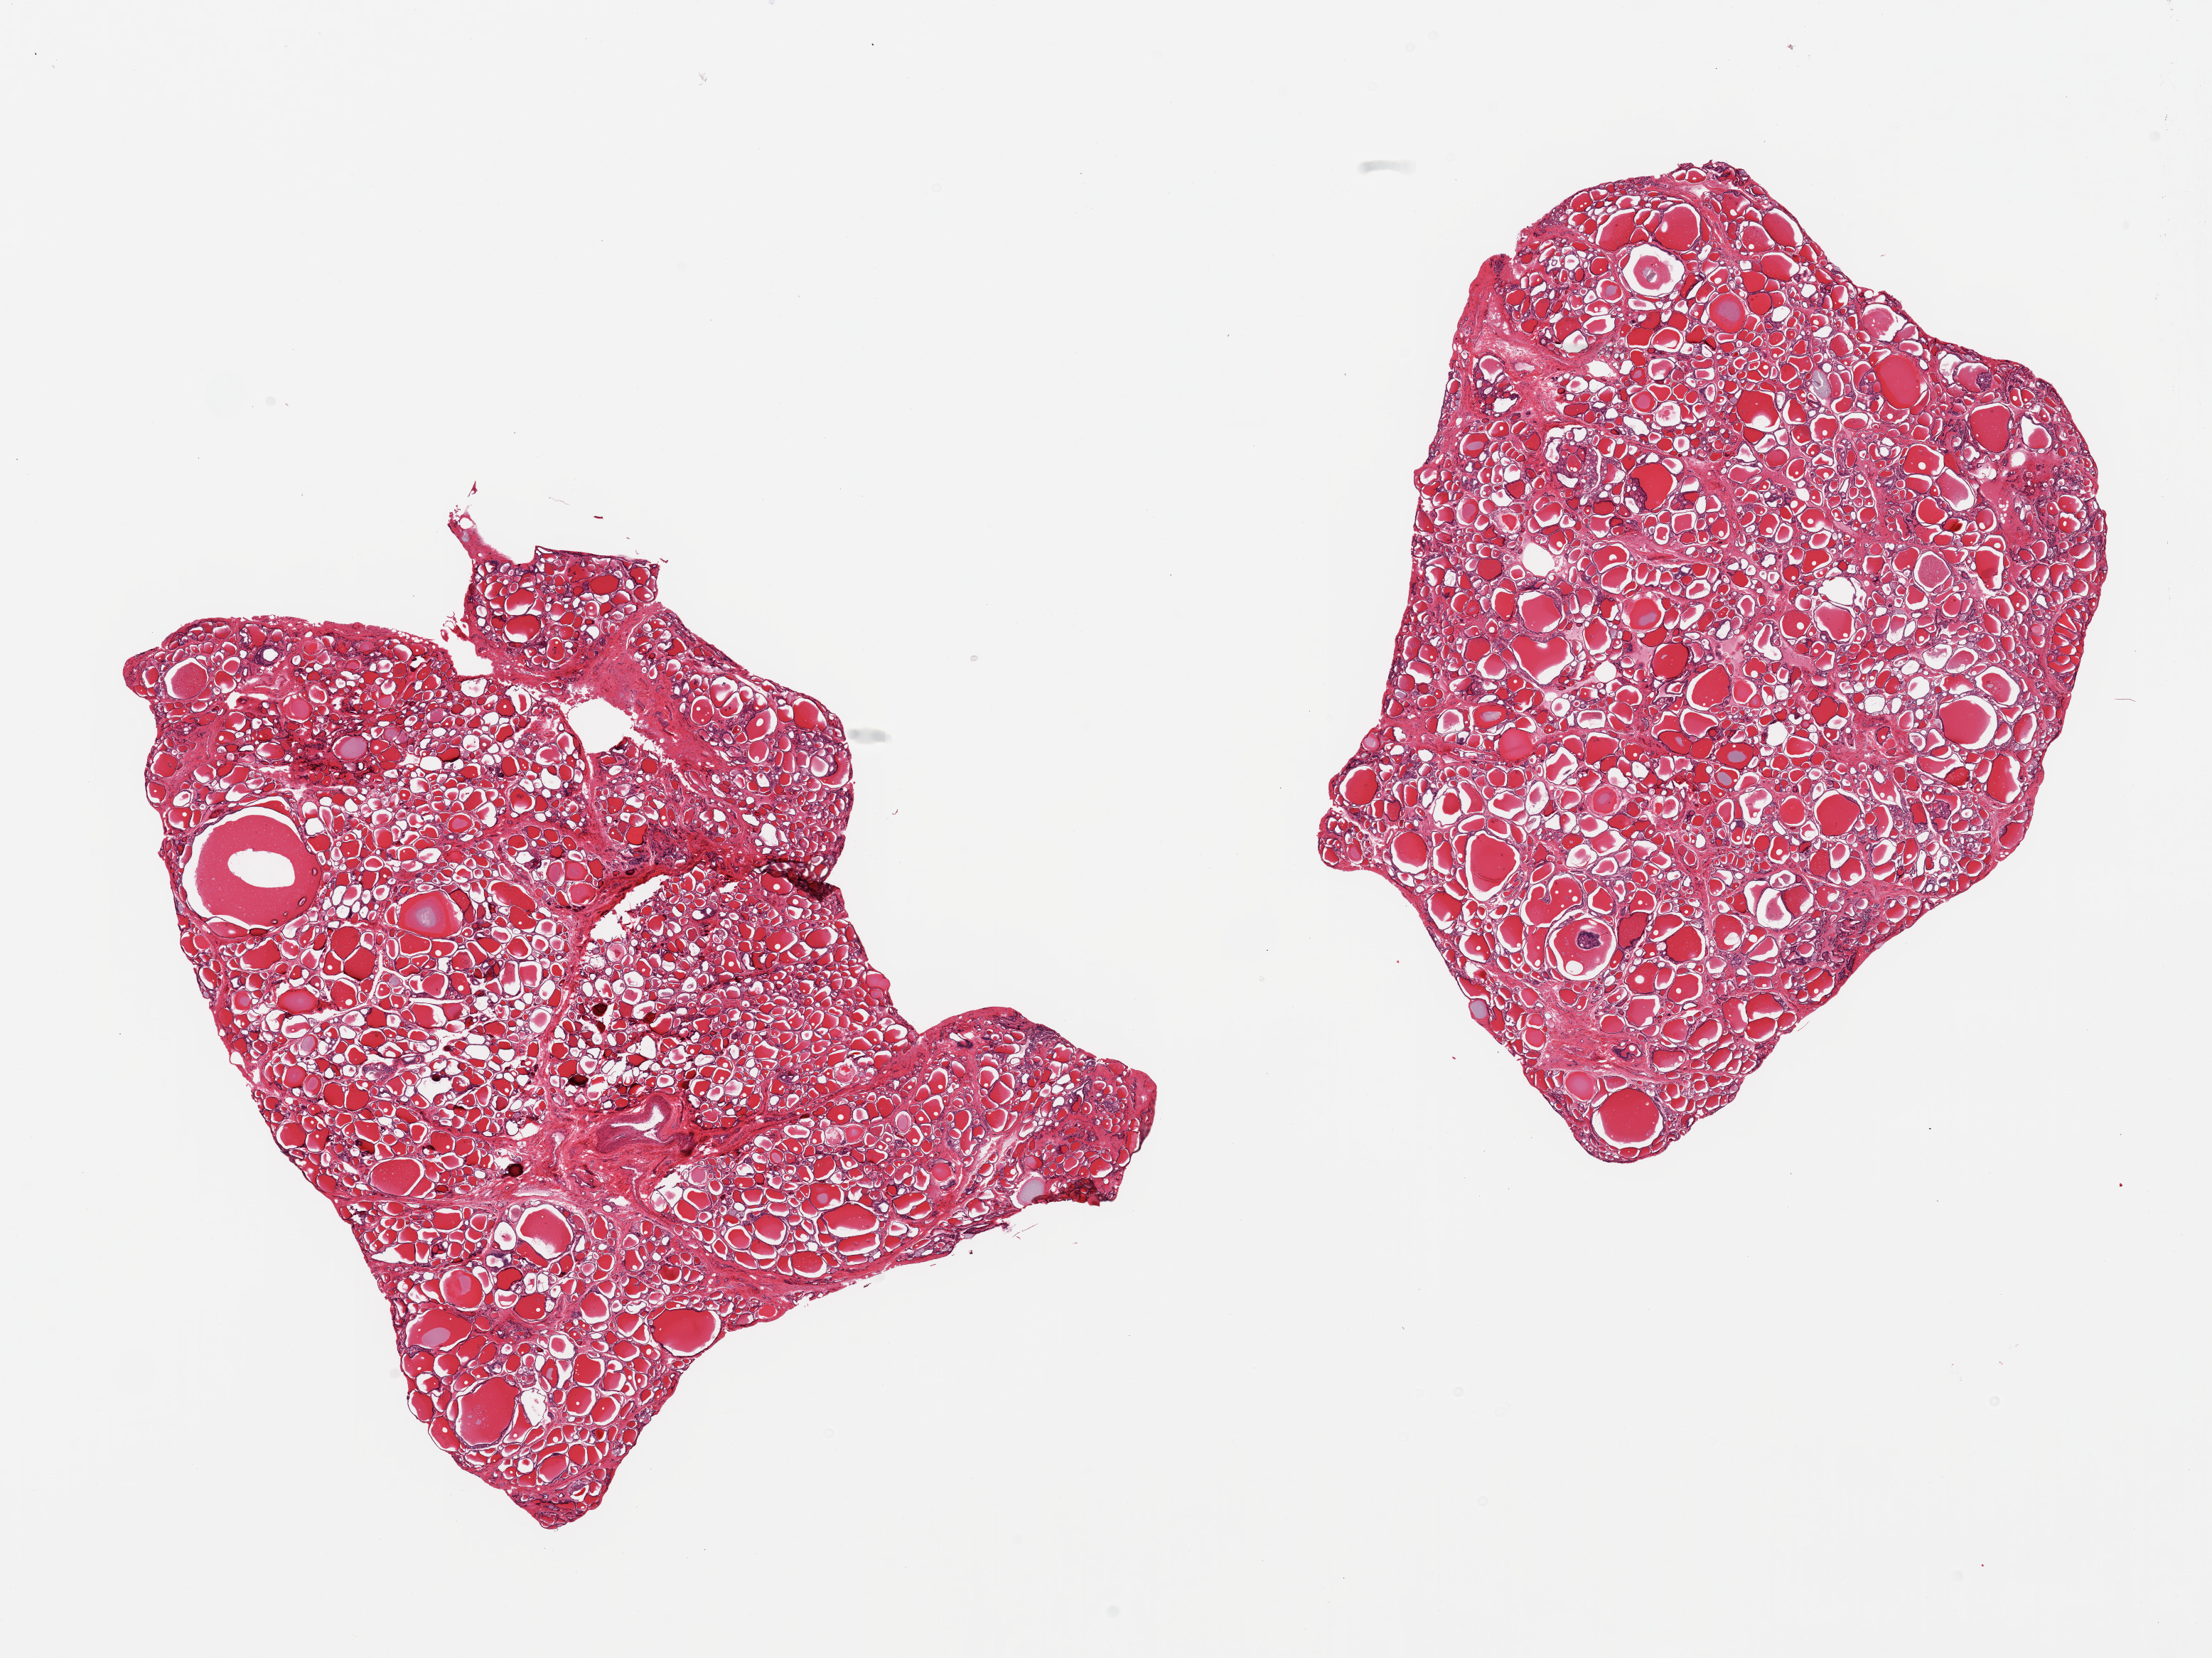
Digitized H&E-stained section — shown as a low-resolution overview of the whole scanned area (about 24.6 x 18.4 mm); PAXgene-fixed paraffin-embedded (PFPE) section; sampled site (target tissue): thyroid; tissue donor sample. Donor: female.
• review note (as recorded): 2 pieces, no significant abnormality